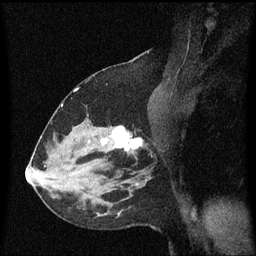
Breast MRI (dynamic contrast-enhanced), one sagittal slice. Slice 37 of 60 in the series (ordered by position). Dynamic contrast-enhanced series, image 2 of 3 at this slice position (ordered by acquisition). 1.5 T. TE 4.2 ms, TR 8.4 ms. 2 mm slice thickness. 256 × 256 image matrix, field of view 200 × 200 mm. Patient: female, 37 years. Case-level facts recorded for this patient, not image findings: setting: breast cancer imaged before/during neoadjuvant chemotherapy; receptor status: HR-positive, HER2-negative.
Structures marked on this image (semi-automatically segmented with operator editing):
- analysis volume of interest (the breast-tissue region the enhancement analysis was run in; not a lesion): bounding box <95,126,151,171> (left, top, right, bottom; pixels)
- tumour enhancement mask (voxels above the 70 % enhancement threshold inside the analysis volume of interest): <102,126,144,153>